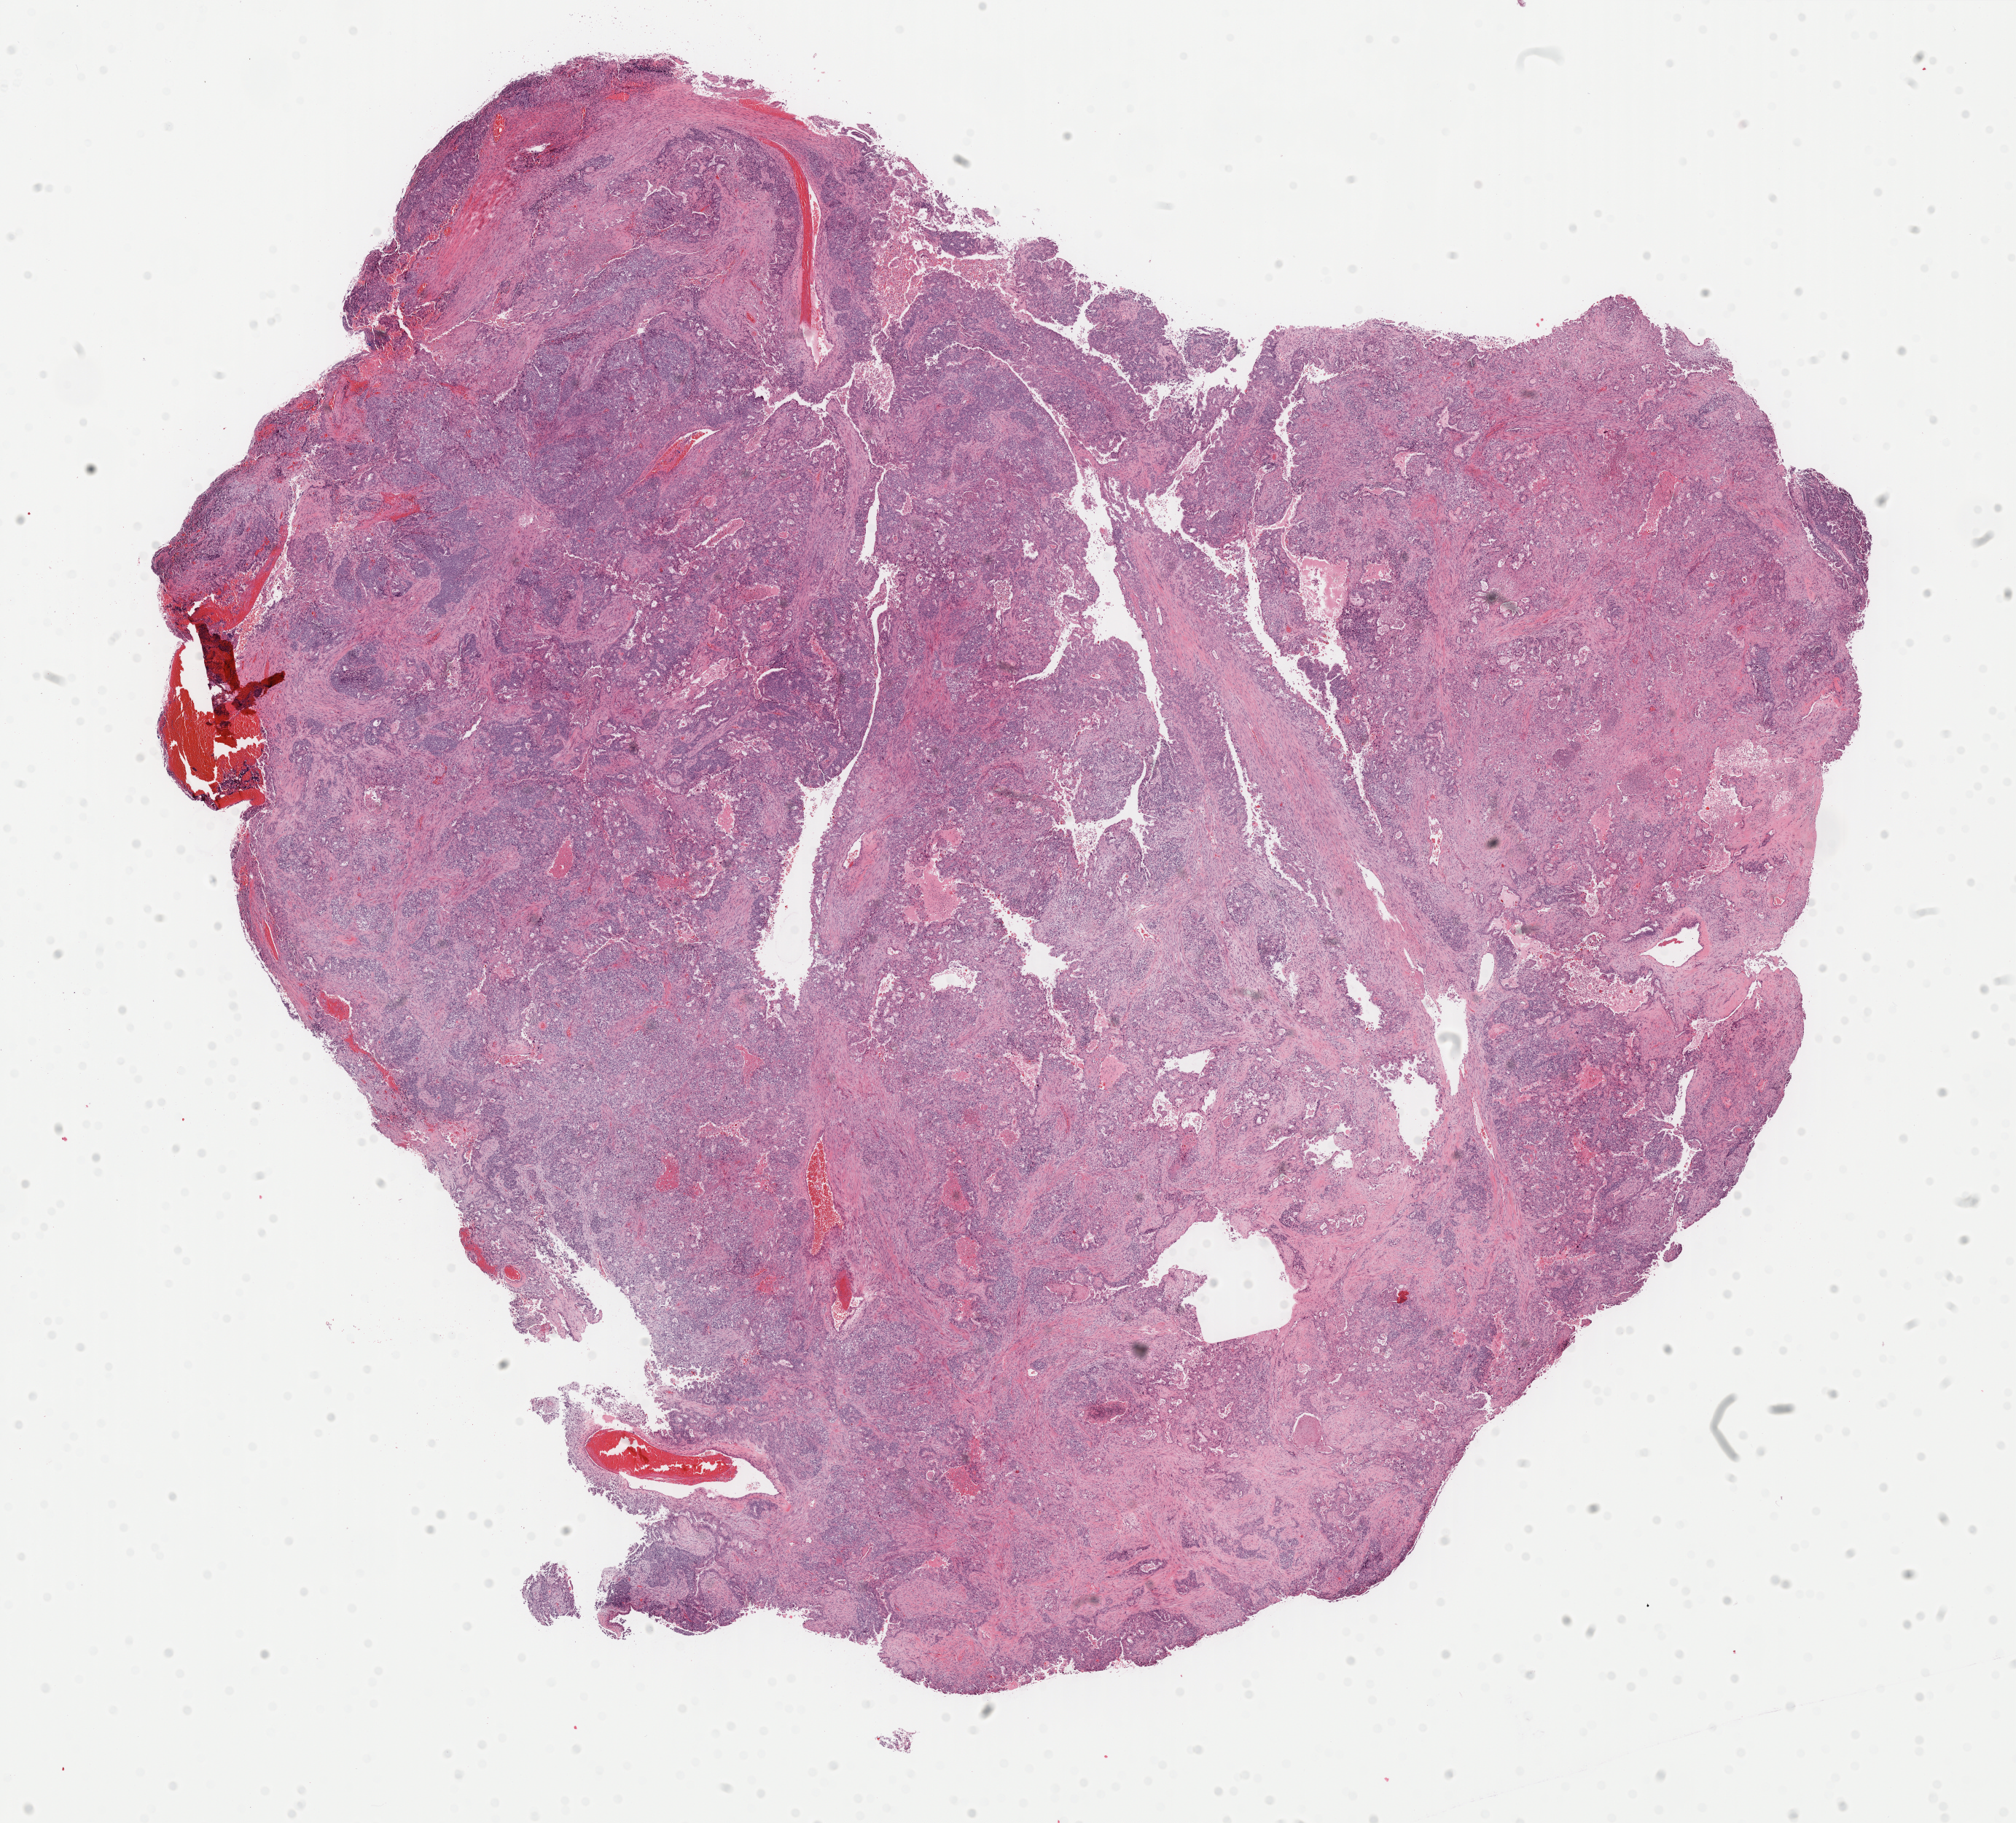
Digitized Hematoxylin and eosin (H&E) stained tissue section (whole slide) — low-resolution overview of the scanned area, about 21.9 x 19.8 mm (from a 40x scan). FFPE section. Primary tumour sample from the uterus. Patient: female, age at initial diagnosis 55 years. Histologic grade: G3 (poorly differentiated).
* histologic diagnosis: Endometrioid adenocarcinoma, NOS (endometrium)
* FIGO stage: IA